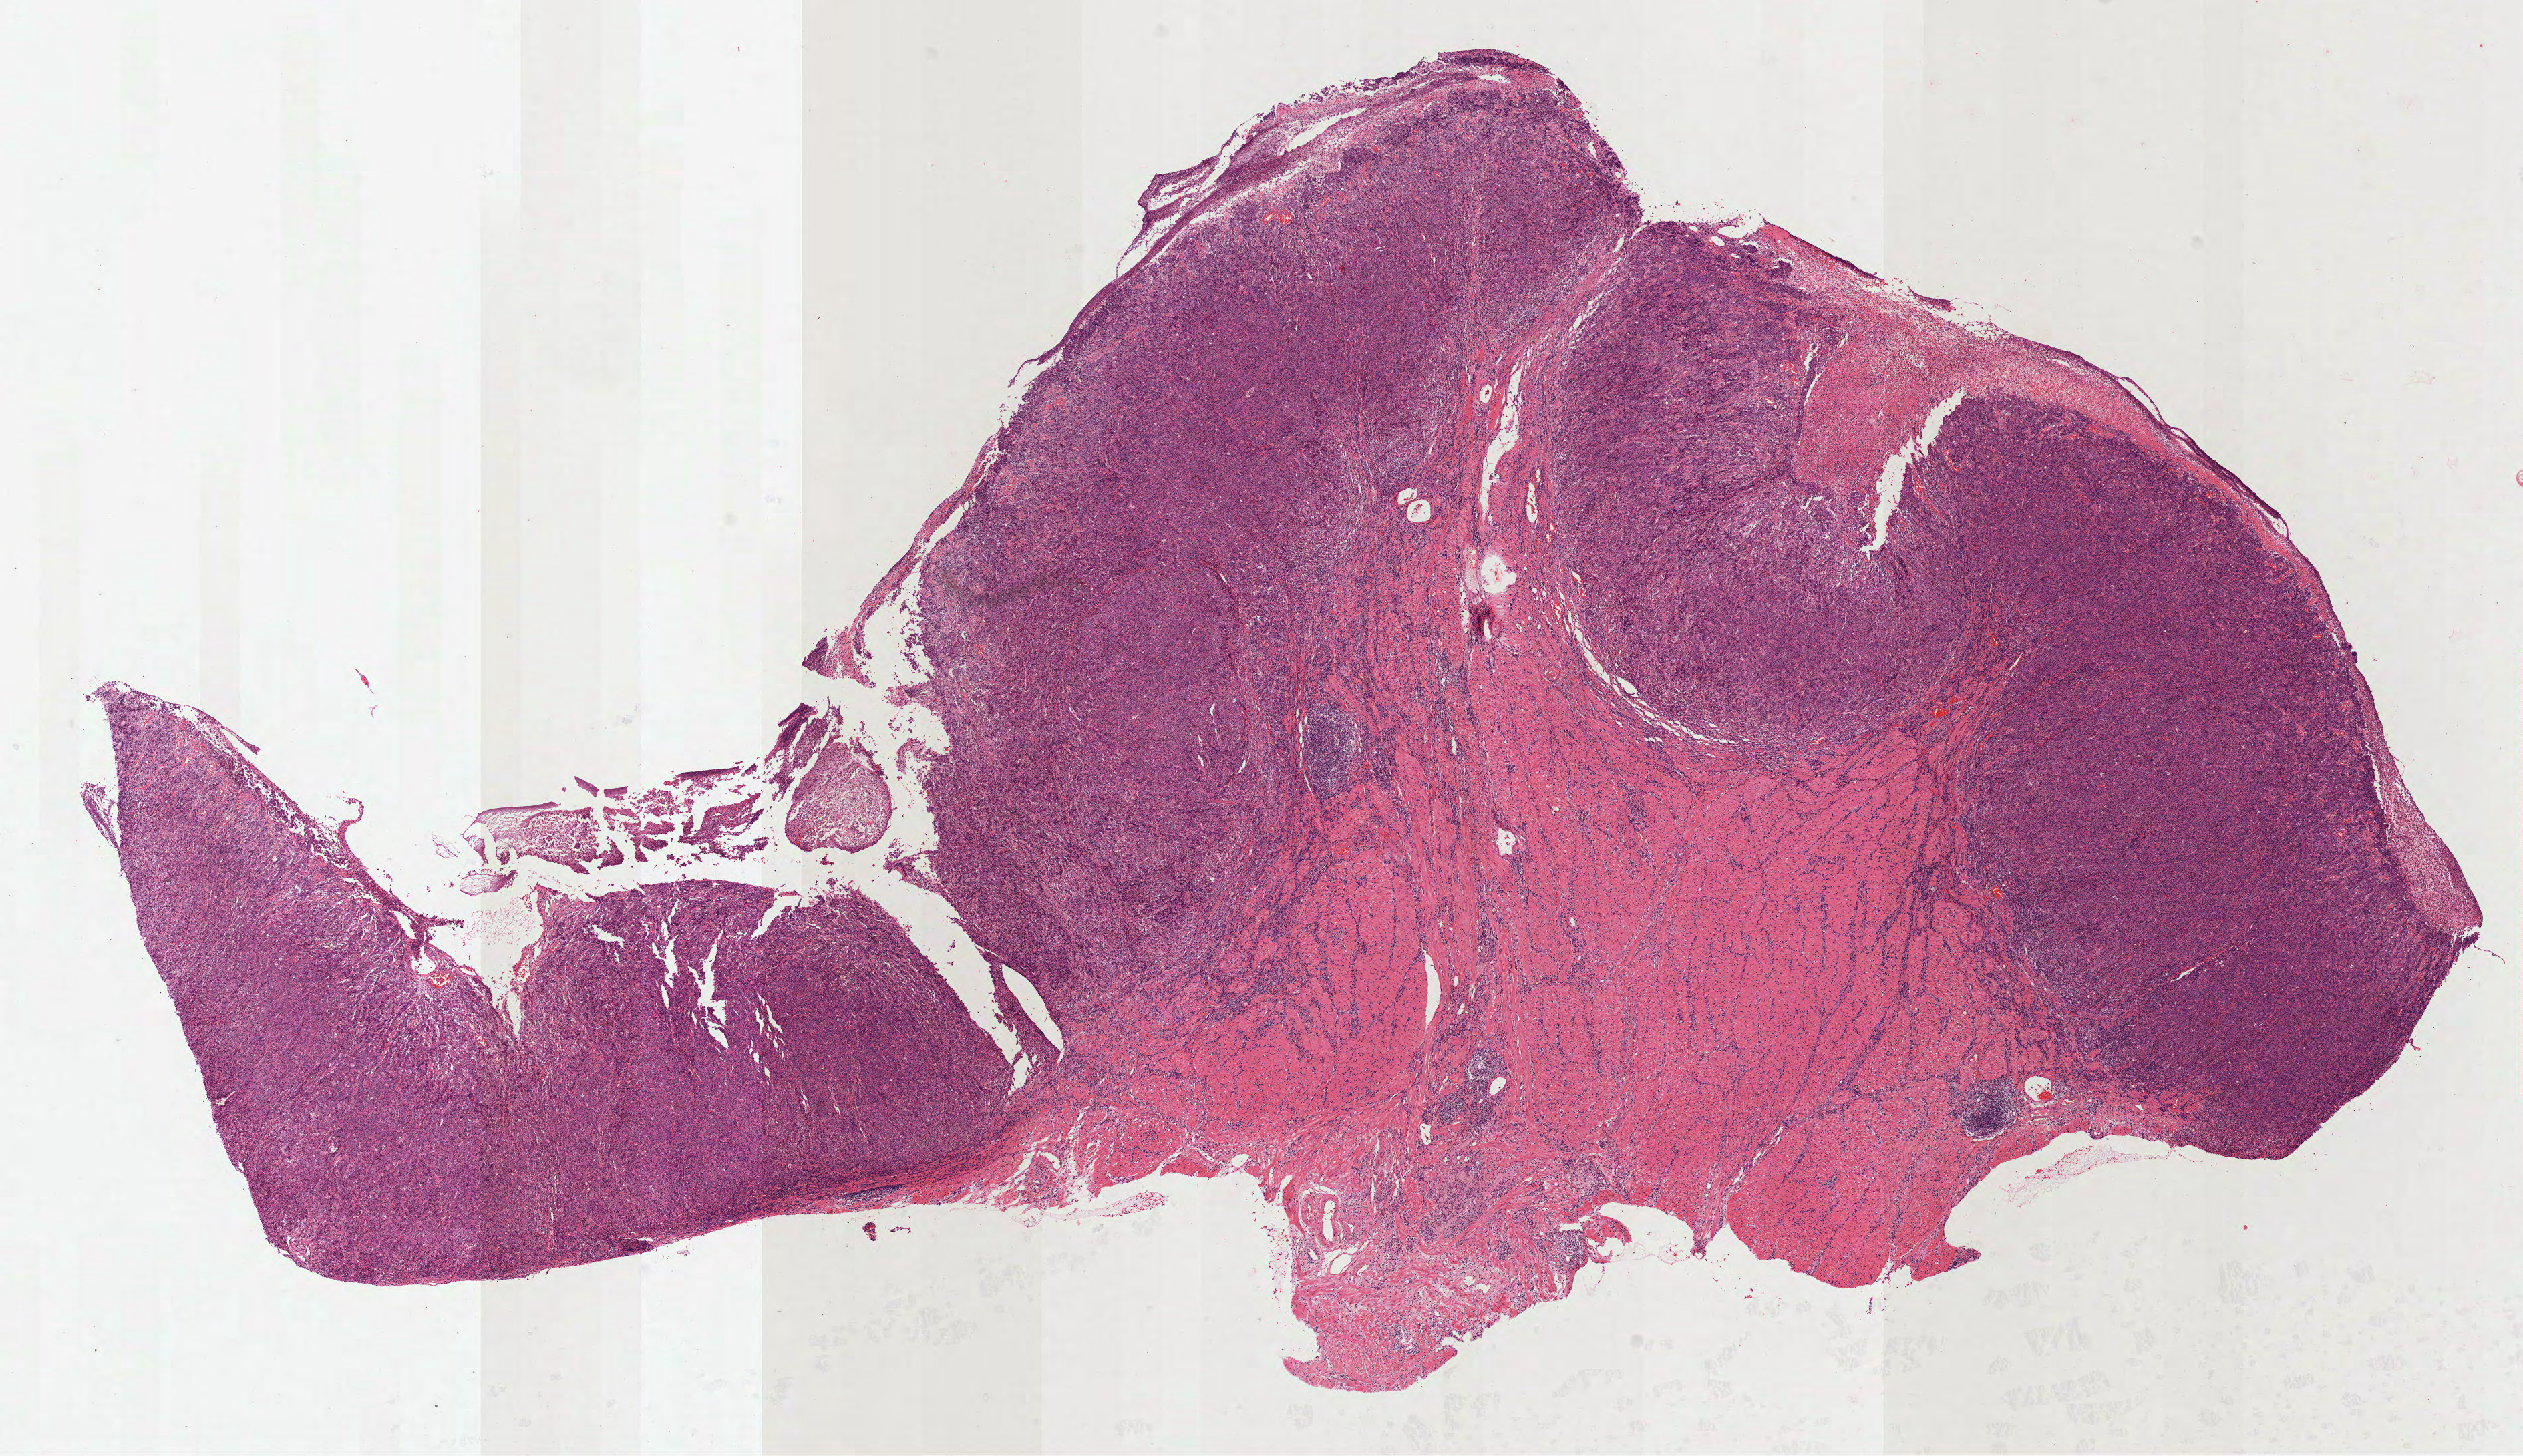
H&E whole-slide image — a low-resolution overview of the entire scanned area, about 15.2 x 8.8 mm. Formalin-fixed paraffin-embedded (FFPE) diagnostic section. Sample: primary tumour, stomach. Female patient; age at initial diagnosis 73 years. Histologic grade: G3 (poorly differentiated).
- histologic diagnosis: Adenocarcinoma, NOS (fundus of stomach)
- AJCC pathologic stage: IB
- lymph nodes positive (case pathology): 0 of 11 examined